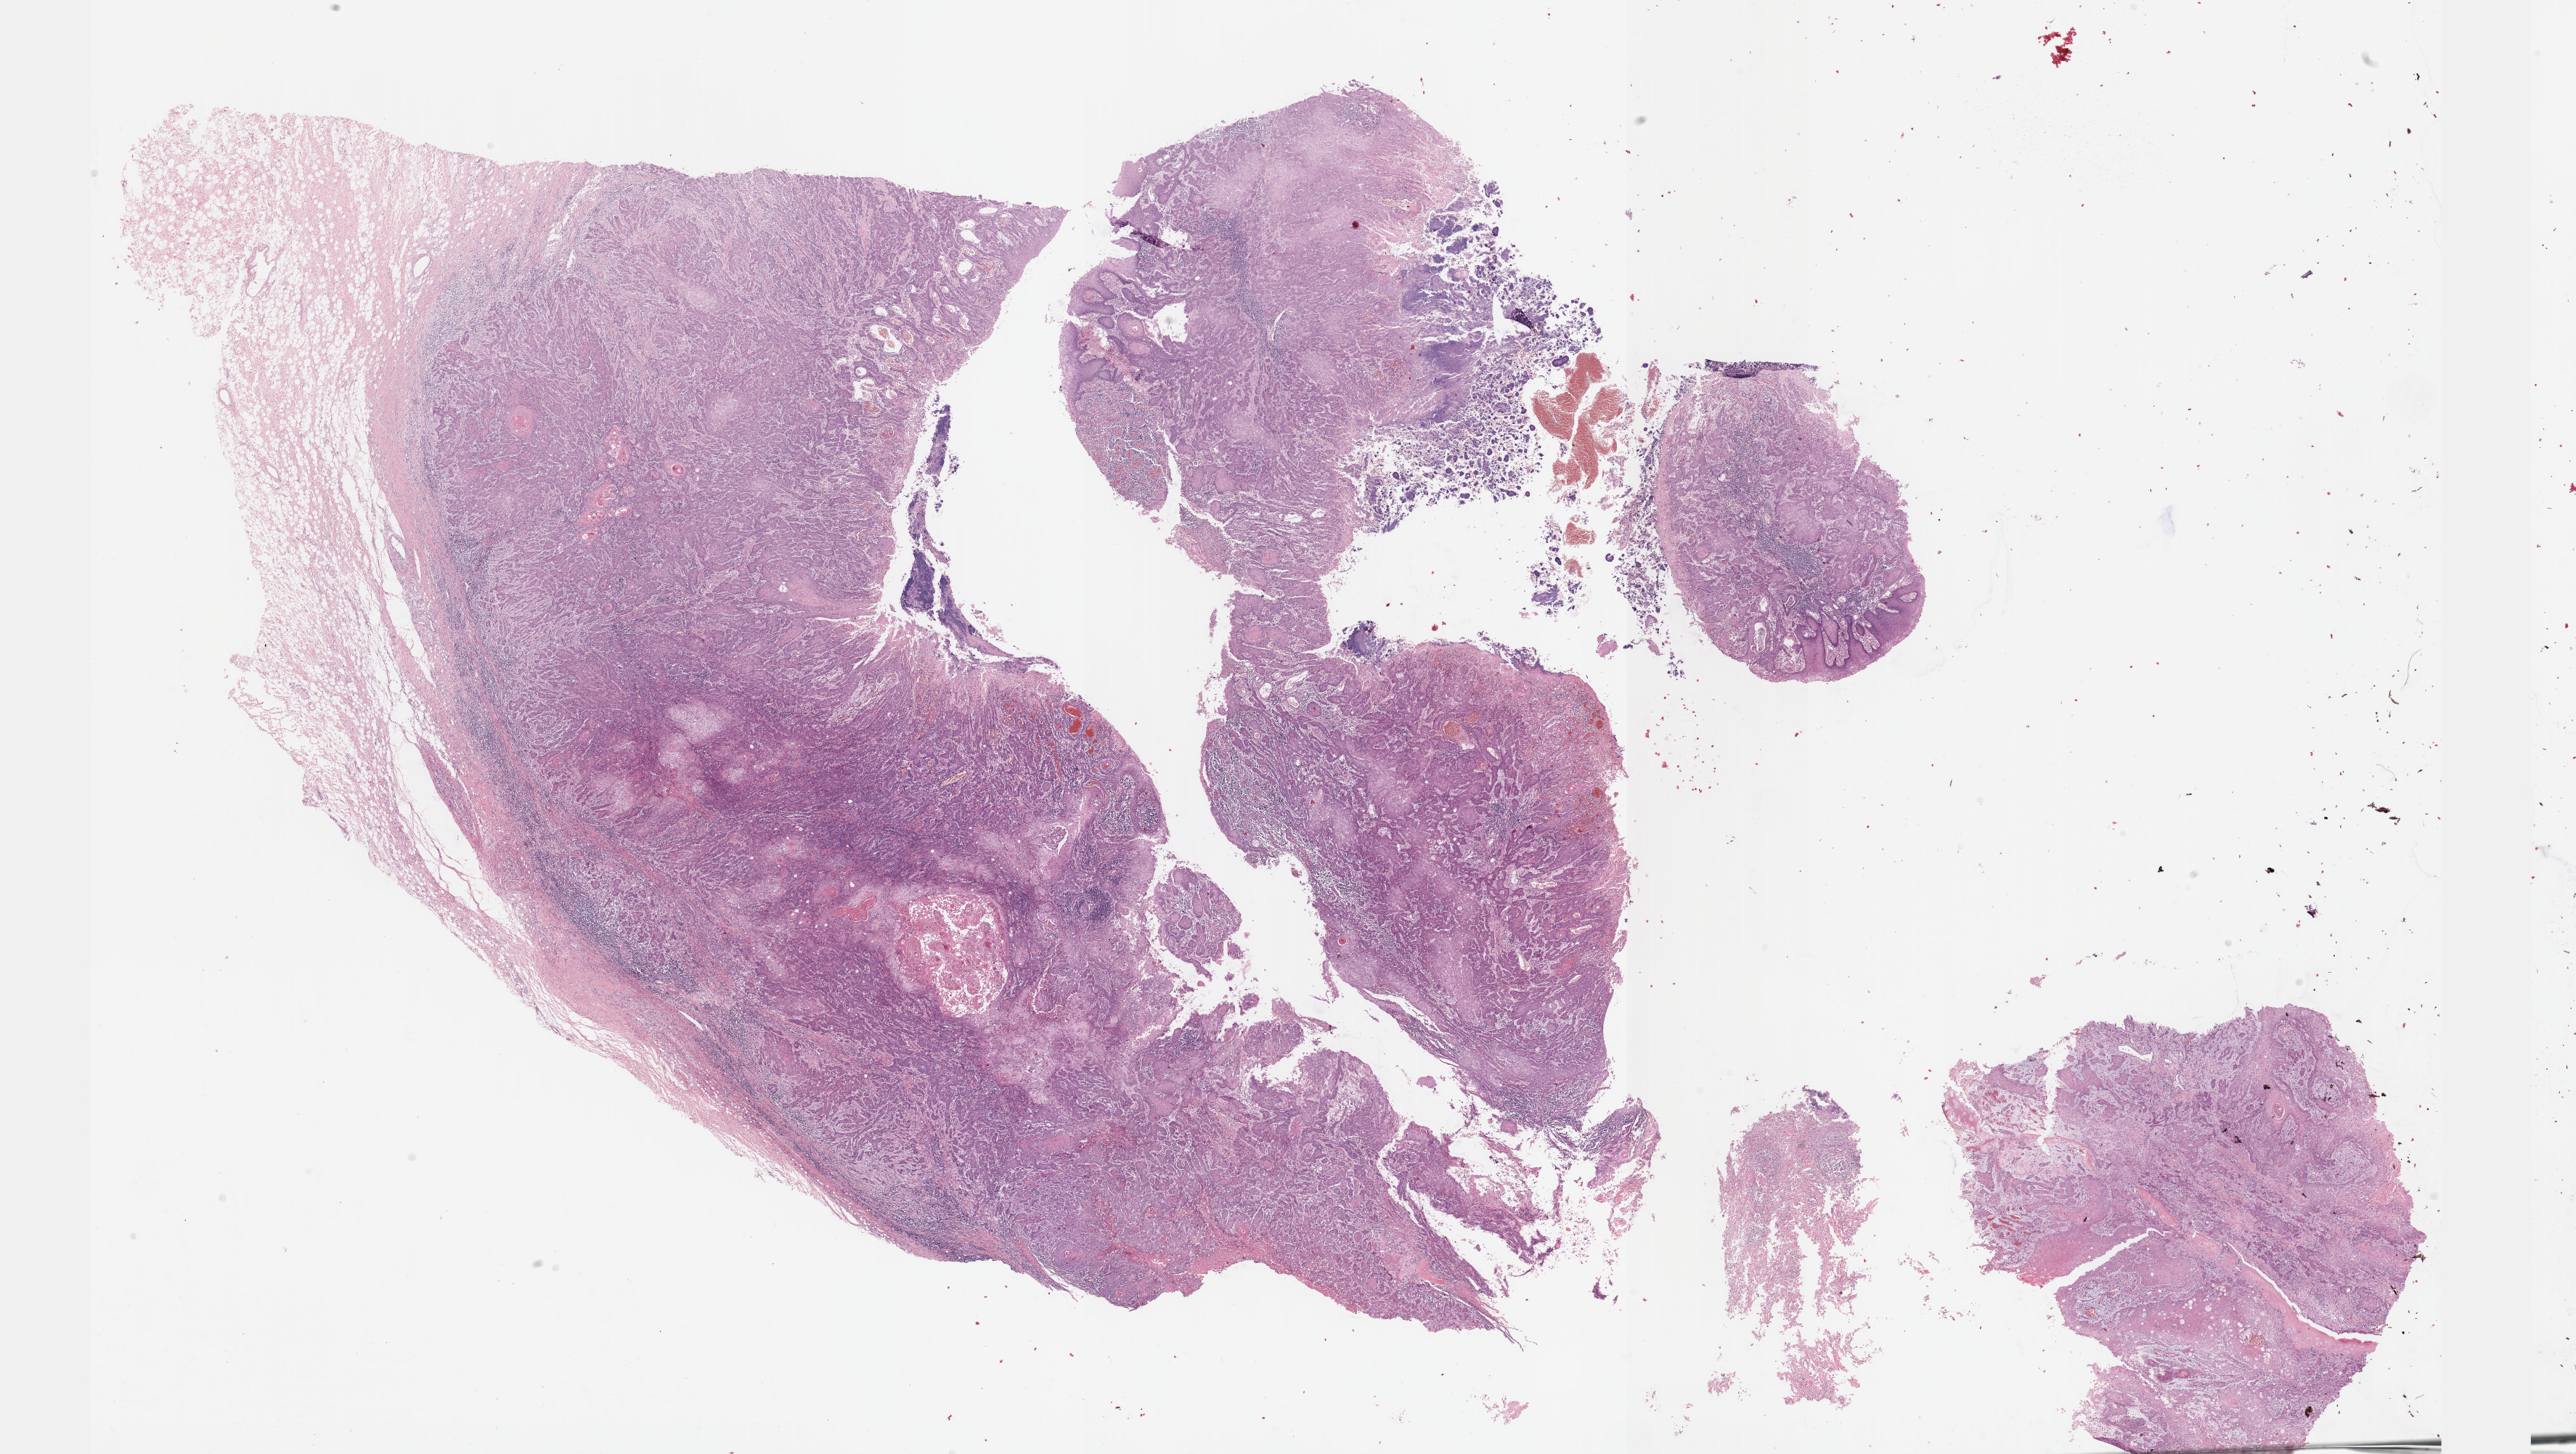
Hematoxylin and eosin (H&E) stained whole-slide image, shown as a low-resolution overview of the whole scanned area (about 28.7 x 16.2 mm, from a 40x scan). Formalin-fixed paraffin-embedded (FFPE) diagnostic section. Head and neck, primary tumour sample. Male, age 62 years at initial diagnosis. Histologic grade: G2 (moderately differentiated).
Diagnosis: Squamous cell carcinoma, NOS (larynx, NOS). AJCC pathologic stage: IVA (7th edition).